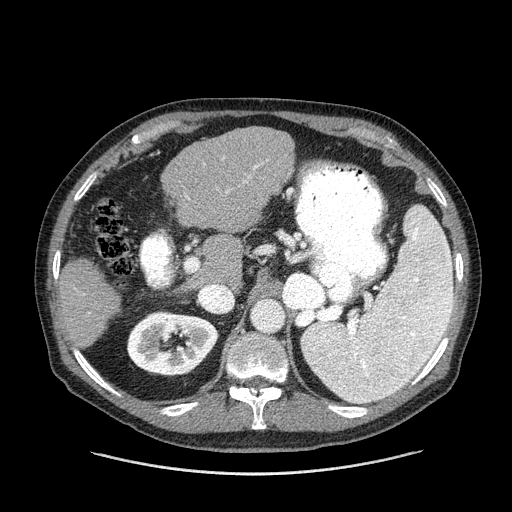
Contrast-enhanced abdominal CT (liver protocol), one axial slice; slice 80 of 180 in the series (ordered by position); reconstruction kernel STANDARD; 120 kVp; one of 2 acquisitions stored at this slice position; soft-tissue window (W 400 / L 40 HU); 2.5 mm slice thickness; 512 × 512 image matrix, field of view 420 × 420 mm. Case-level facts recorded for this patient, not image findings: diagnosis: hepatocellular carcinoma (patient treated with transarterial chemoembolisation; whether this scan precedes or follows treatment is not stated here); TNM stage (as recorded): Stage-II; Child-Pugh class: A; tumour nodularity: multinodular; tumour size: 2.8 cm.
Structures marked on this image (semi-automatically segmented with operator editing):
- liver parenchyma outside the tumour (the mass and vessels are separate outlines, so this box may not span the whole liver): box from (x=56, y=126) to (x=294, y=348) px
- liver vessels: (x=185, y=157)–(x=263, y=199)